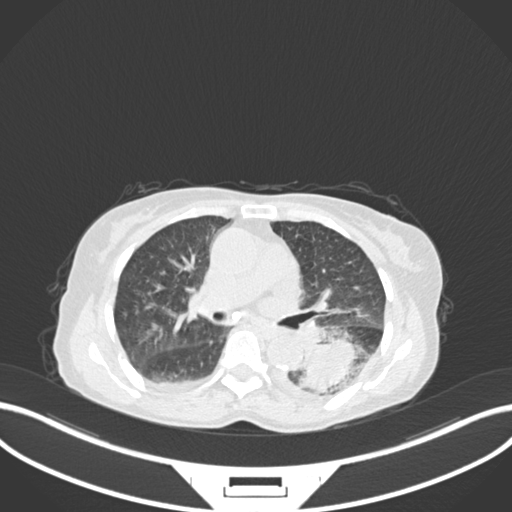
Chest CT, one axial slice. Slice 99 of 233 in the series (ordered by position). 120 kVp. Lung window (W 1500 / L -600 HU). 1 mm slice thickness. 512 × 512 image matrix. Patient: female, 78 years. From the clinical record (not read from this slice): clinical TNM (as recorded): T3 N0 M1.
Outlined on this slice (rectangle marked by the reading radiologist):
- lung tumour (recorded histology: squamous cell carcinoma): bounding box <294,336,366,396> (left, top, right, bottom; pixels)